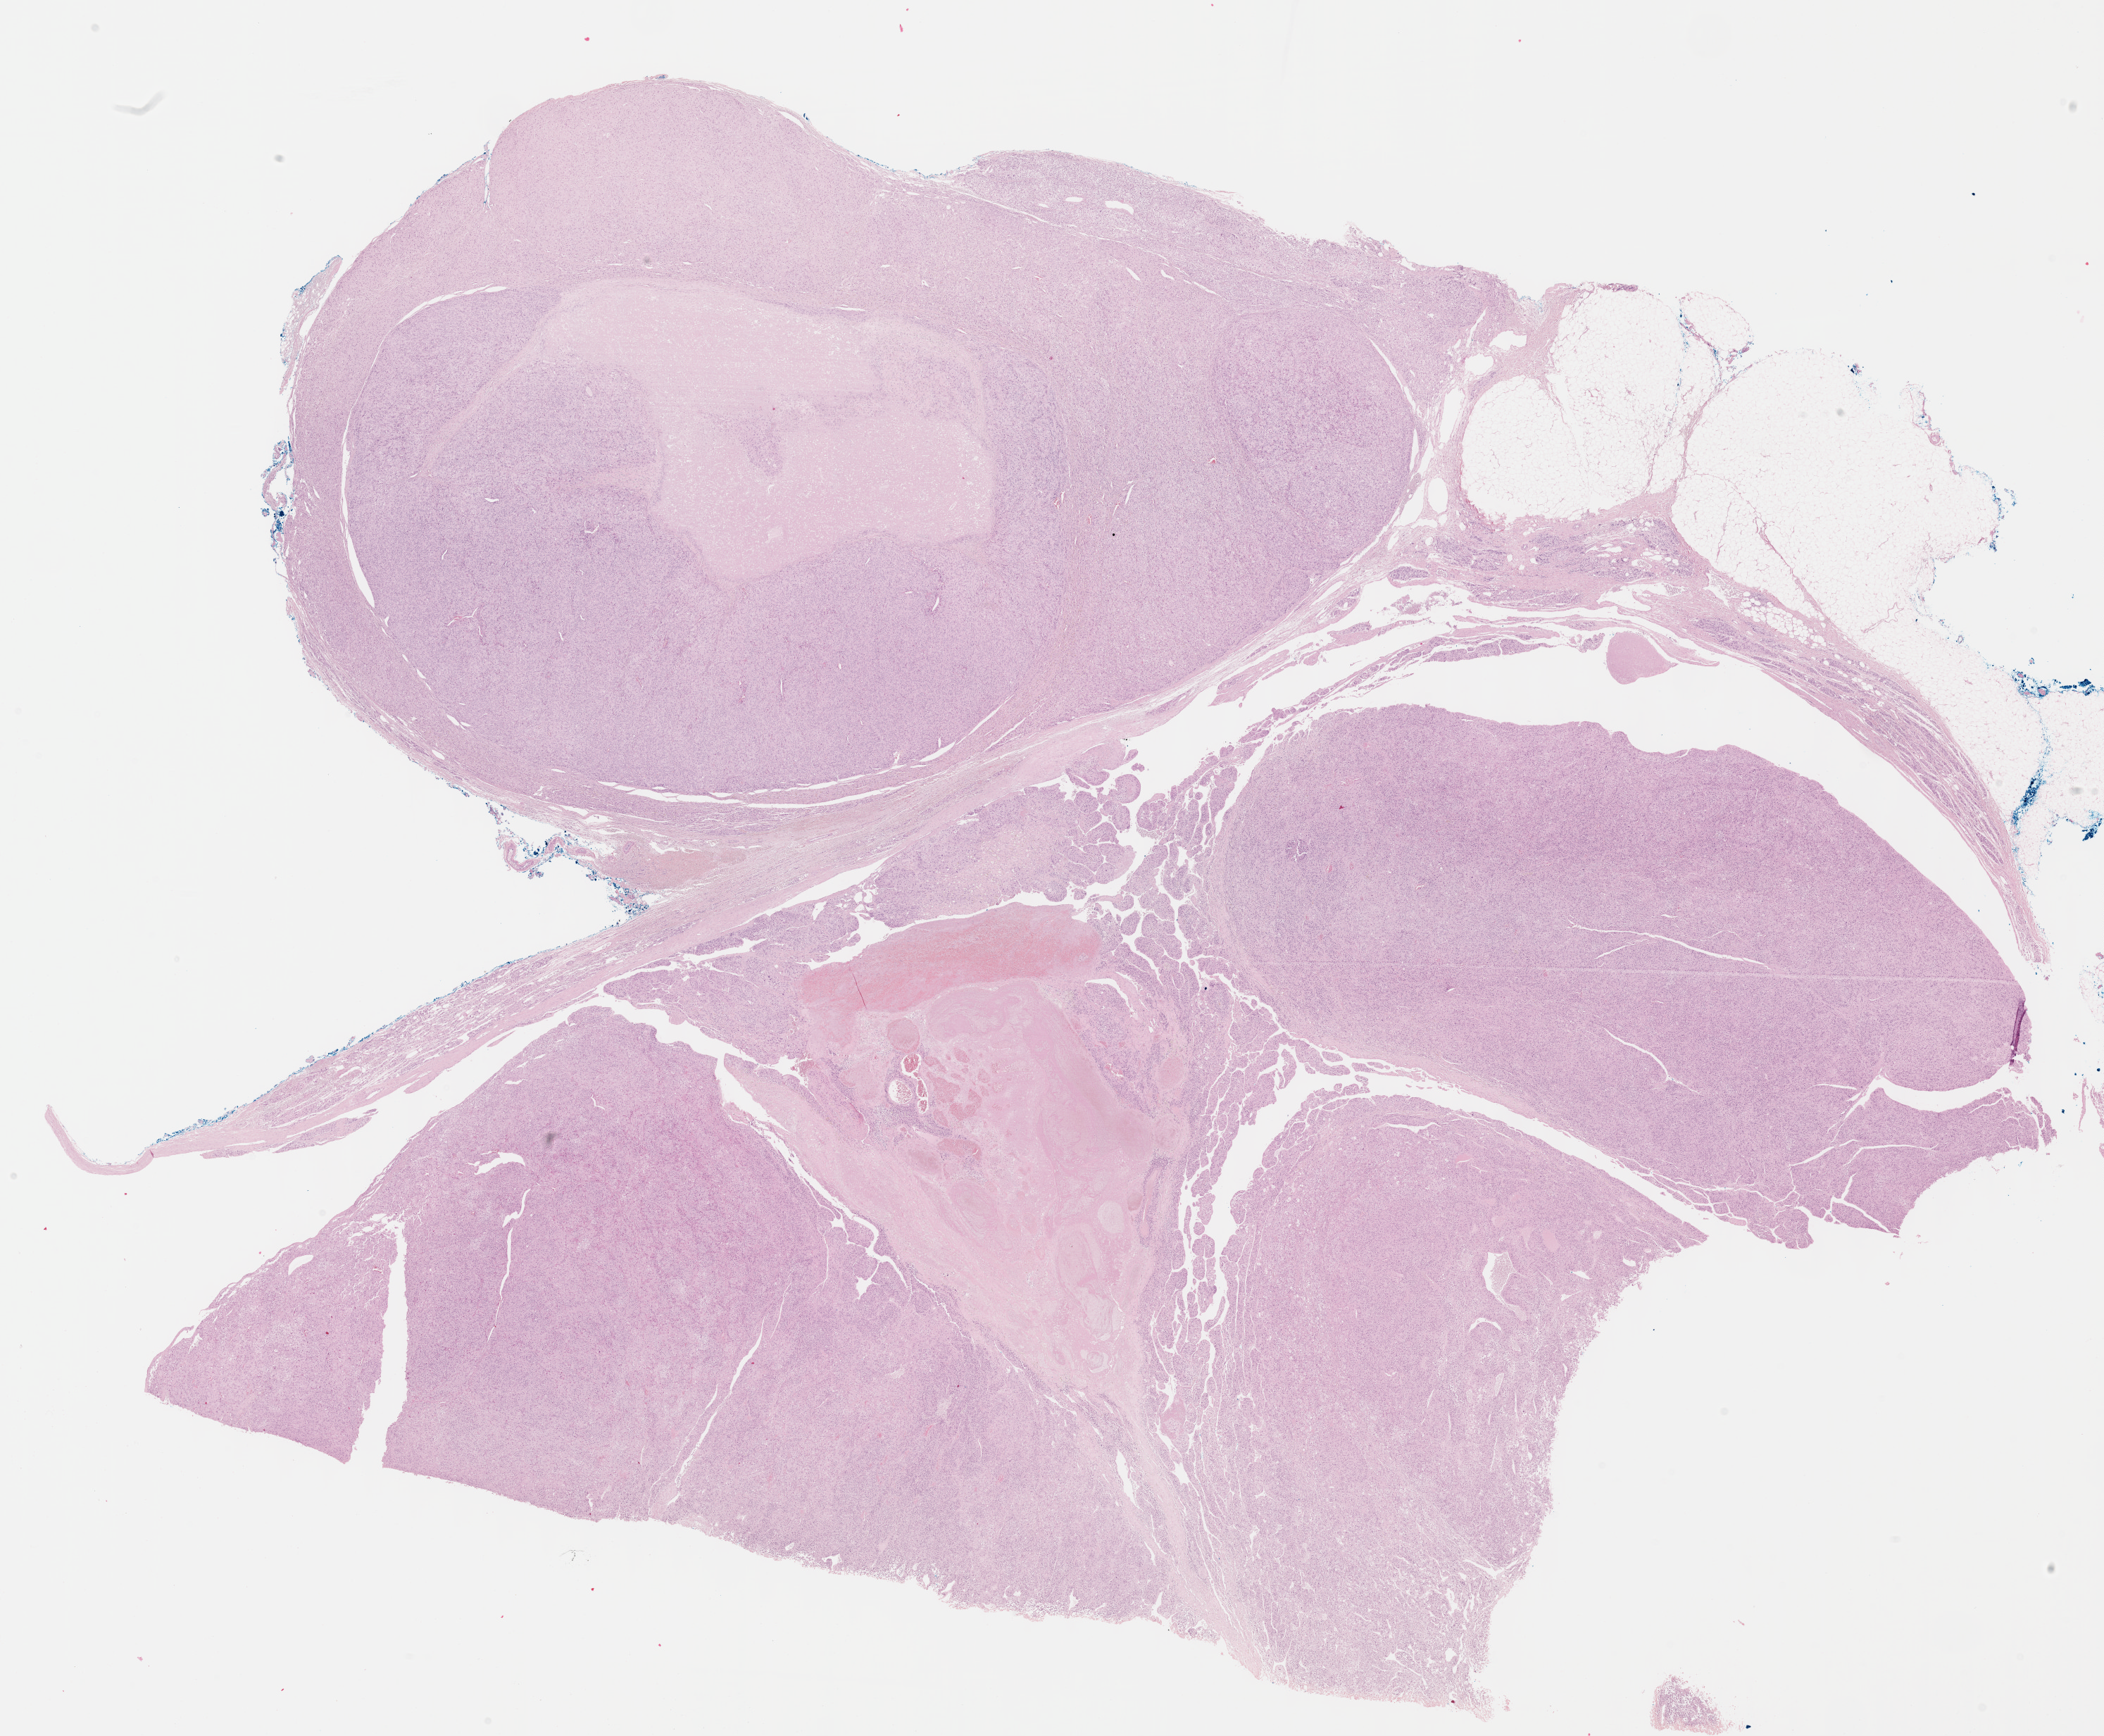
H&E whole-slide image, whole scanned area (about 24.1 x 19.9 mm, slide scanned at 40x) shown as a low-resolution overview; formalin-fixed paraffin-embedded (FFPE) diagnostic section; adrenal cortex, primary tumour sample. Female patient; age at initial diagnosis 17 years.
Diagnosis: Adrenal cortical carcinoma (cortex of adrenal gland).